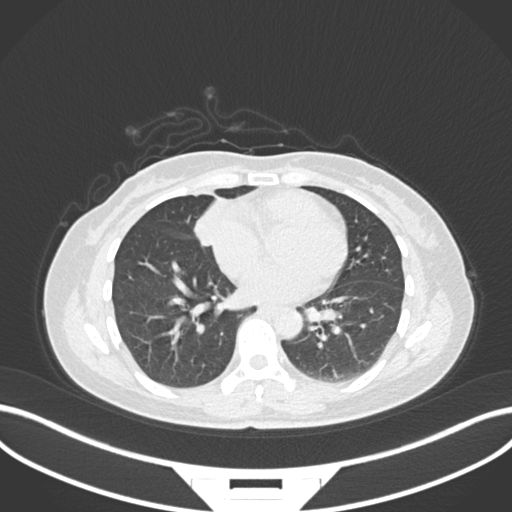
Chest CT, one axial slice. Slice 63 of 171 in the series (ordered by position). Lung window (W 1500 / L -600 HU). 1 mm slice thickness. 512 × 512 image matrix. Female patient, age 43 years. Case-level facts recorded for this patient, not image findings: clinical TNM (as recorded): T1c N3 M1; histopathological grade: G1.
Annotated regions visible in this slice (rectangle marked by the reading radiologist):
- lung tumour (recorded histology: adenocarcinoma): bounding box (x1, y1, x2, y2) in pixels: (187, 196, 223, 252)